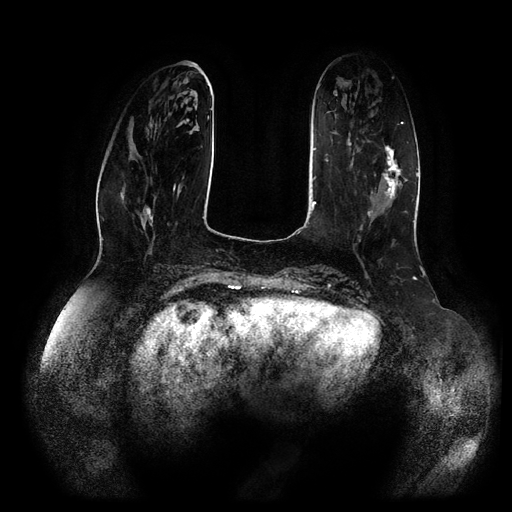
Breast MRI (dynamic contrast-enhanced, multi-phase), one axial slice. Position 31 of 116 along the scan axis. Dynamic contrast-enhanced series, time point 2 of 5 at this slice position (early post-contrast). 1.5 T. TE 2.5 ms, TR 5.2 ms. 512 × 512 image matrix. Patient: female, 66 years.
Outlined on this slice (semi-automatically segmented with operator editing):
- breast lesion (labelled 'tumour' in the annotation; benign lesions carry a separate 'benign' label): bounding box [x1, y1, x2, y2] px = [382, 146, 408, 200]